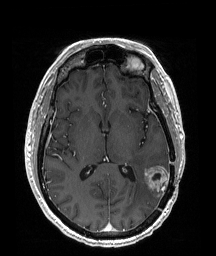
Brain MRI from a brain-tumour surgery series, one axial slice; slice 92 of 192 in the series (ordered by position); T1-weighted post-contrast; 1 mm slice thickness; 216 × 256 image matrix. Case-level facts recorded for this patient, not image findings: histopathology: Glioblastoma; WHO grade: 4; IDH mutation: no.
Structures marked on this image (manually delineated by an expert):
- tumour: box from (x=144, y=166) to (x=170, y=197) px